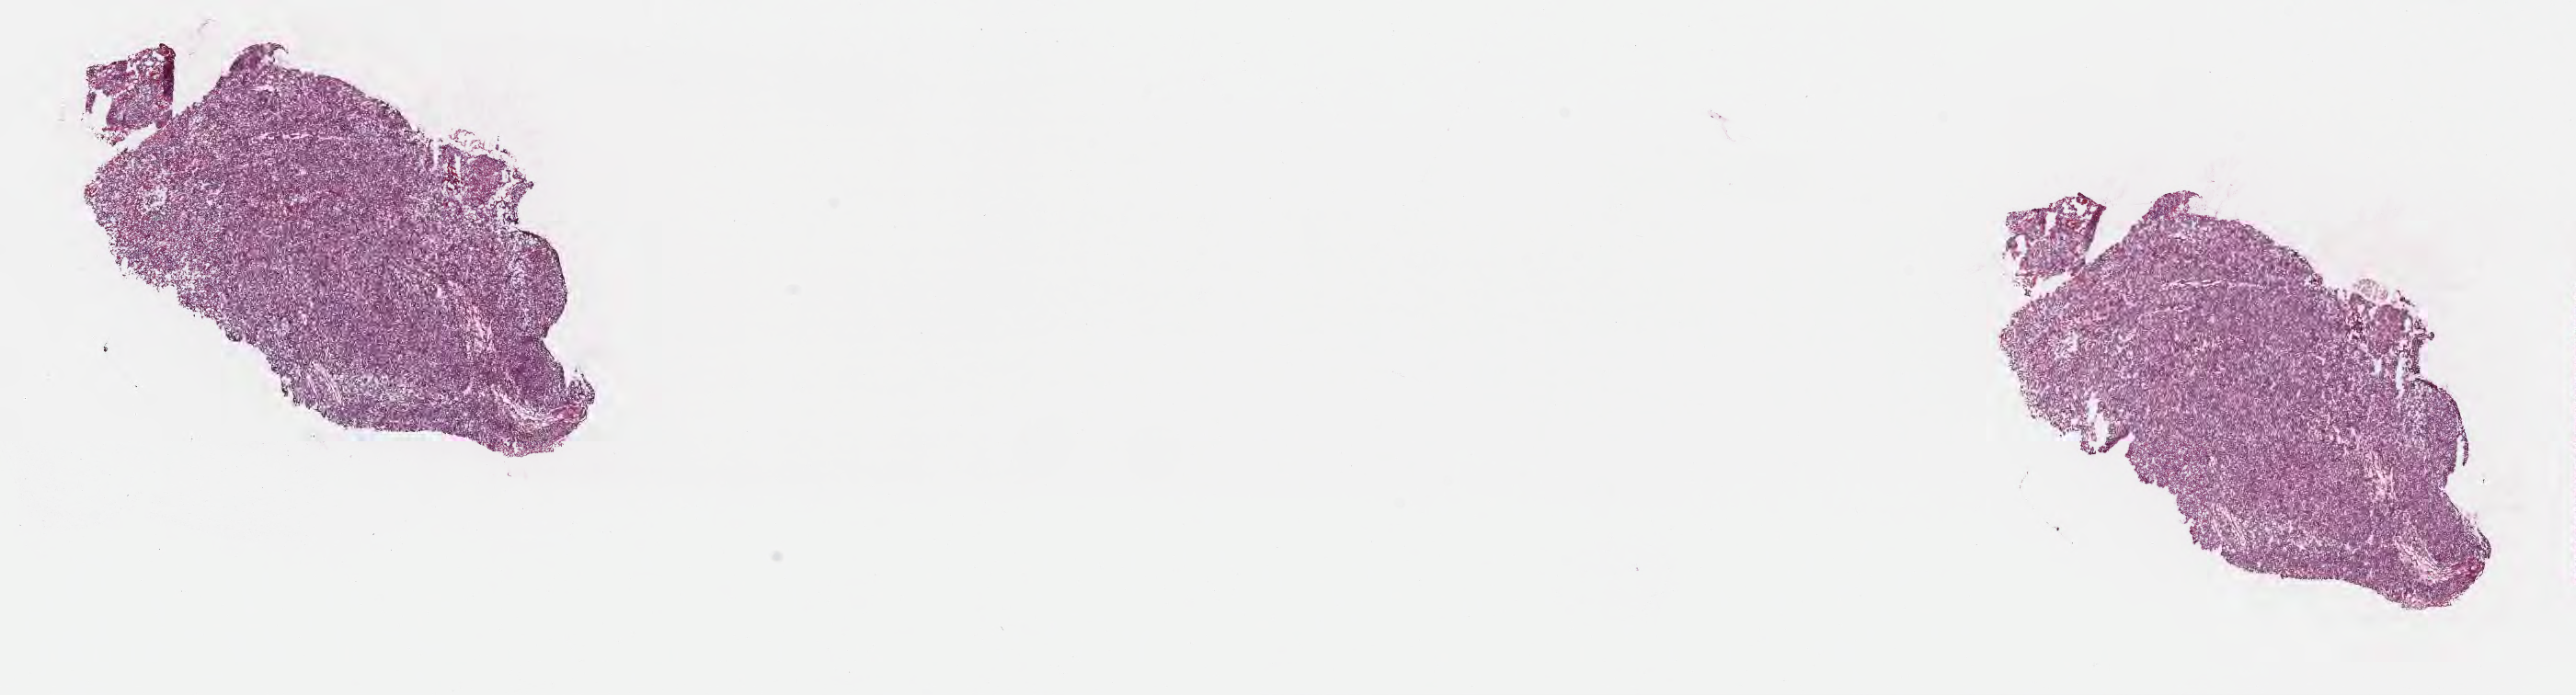
Hematoxylin and eosin (H&E) whole-slide image, whole scanned area (about 22.7 x 6.1 mm) shown as a low-resolution overview. Cryosection. Specimen: primary tumor. Site: brain. Female, age 73 years at initial diagnosis. Slide review estimates, as recorded: tumor cells 88%, tumor nuclei 94%, stromal cells 2%, necrosis 4%, normal cells 6%. Inflammatory infiltration, as recorded: lymphocyte infiltration 0%, monocyte infiltration 0%, neutrophil infiltration 0%.
Histologic diagnosis: Glioblastoma, NOS.